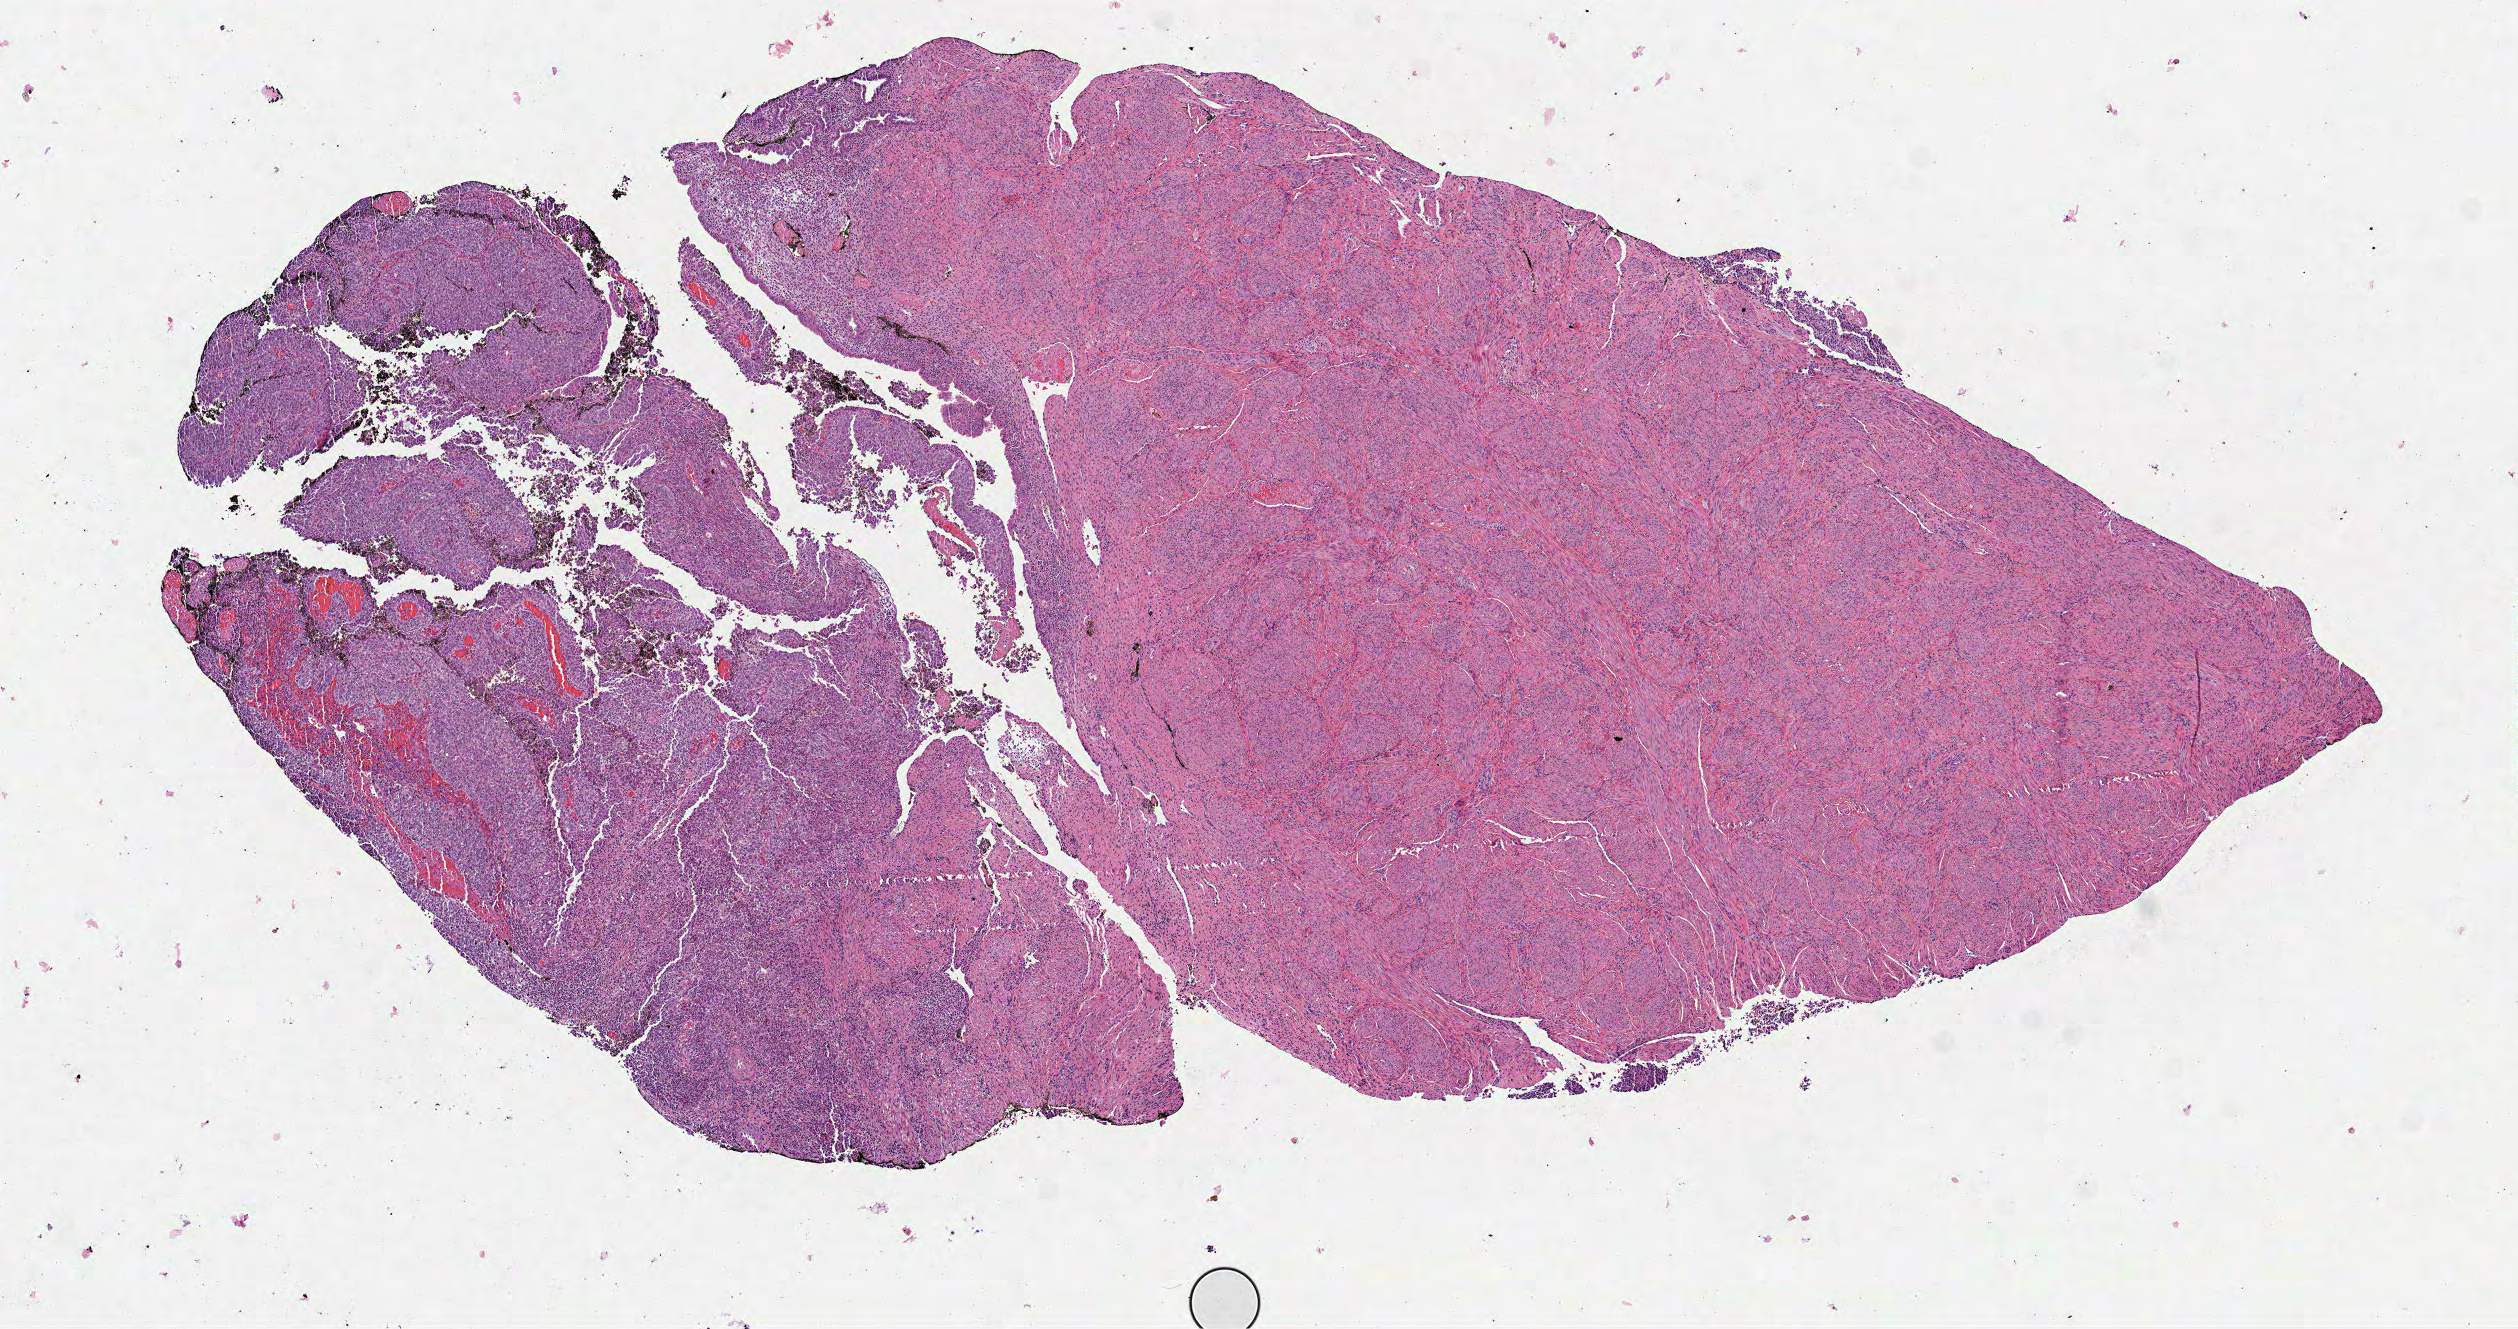
Digitized Hematoxylin and eosin (H&E) stained tissue section (whole slide), whole scanned area (about 10.2 x 5.4 mm) shown as a low-resolution overview; formalin-fixed paraffin-embedded (FFPE) diagnostic section; uterus, primary tumour sample. Female patient; age at initial diagnosis 47 years. Histologic grade: G3 (poorly differentiated).
Lymph nodes positive (case pathology): 0 of 15 examined. FIGO stage: IA. Pathologic diagnosis: Endometrioid adenocarcinoma, NOS (endometrium).